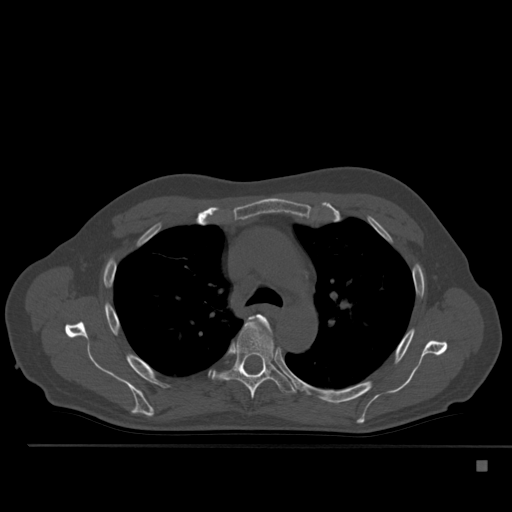
CT including the spine, one axial slice. Position 368 of 517 along the scan axis. Reconstruction kernel Br40s. 120 kVp. Bone window (W 1800 / L 400 HU). 1.5 mm slice thickness. 512 × 512 image matrix, field of view 408 × 408 mm. Patient: male, 70 years. From the clinical record (not read from this slice): primary cancer: renal.
Structures marked on this image (semi-automatic segmentation, software-assisted and operator-edited):
- T4 vertebra: bounding box [x1, y1, x2, y2] px = [257, 315, 270, 329]
- T5 vertebra: [212, 320, 296, 400]